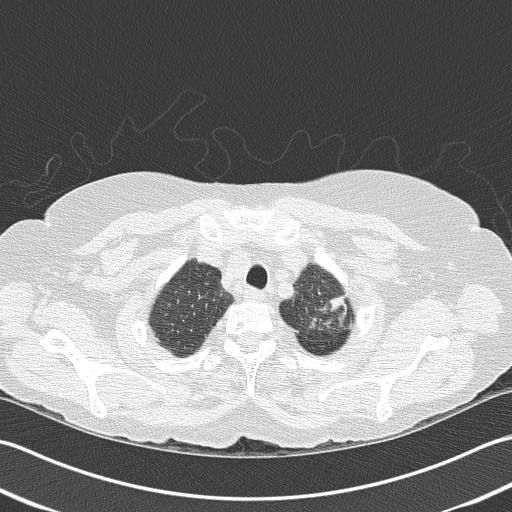
Chest CT (low-dose screening protocol), one axial image. First (baseline) screen. Lung window (W 1500 / L -600 HU). 2 mm slice thickness. 512 × 512 image matrix. Female, age 68 years at enrolment.
Expert reader's lesion annotation, box from (x=289, y=277) to (x=363, y=344) px. No non-calcified nodule or mass ≥4 mm was recorded by the screening reader at this exam. Official screen result: negative screen, minor abnormalities not suspicious for lung cancer. Participant outcome: lung cancer diagnosed 763 days after this screen — adenocarcinoma, NOS, left upper lobe, poorly differentiated (G3), stage IB (AJCC 6th edition), 50 mm at pathology.